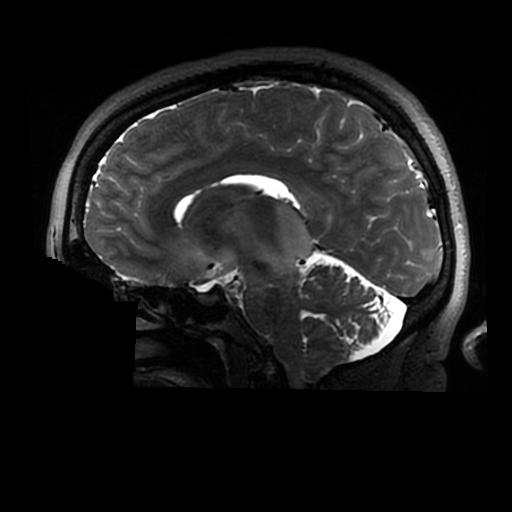
Brain MRI from a brain-tumour surgery series, one sagittal slice. Slice 167 of 320 in the series (ordered by position). 512 × 512 image matrix, field of view 240 × 240 mm. From the clinical record (not read from this slice): histopathology: Astrocytoma; WHO grade: 2; IDH mutation: yes.
Annotated regions visible in this slice (expert manual segmentation):
- tumour: bounding box (x1, y1, x2, y2) in pixels: (207, 202, 316, 276)